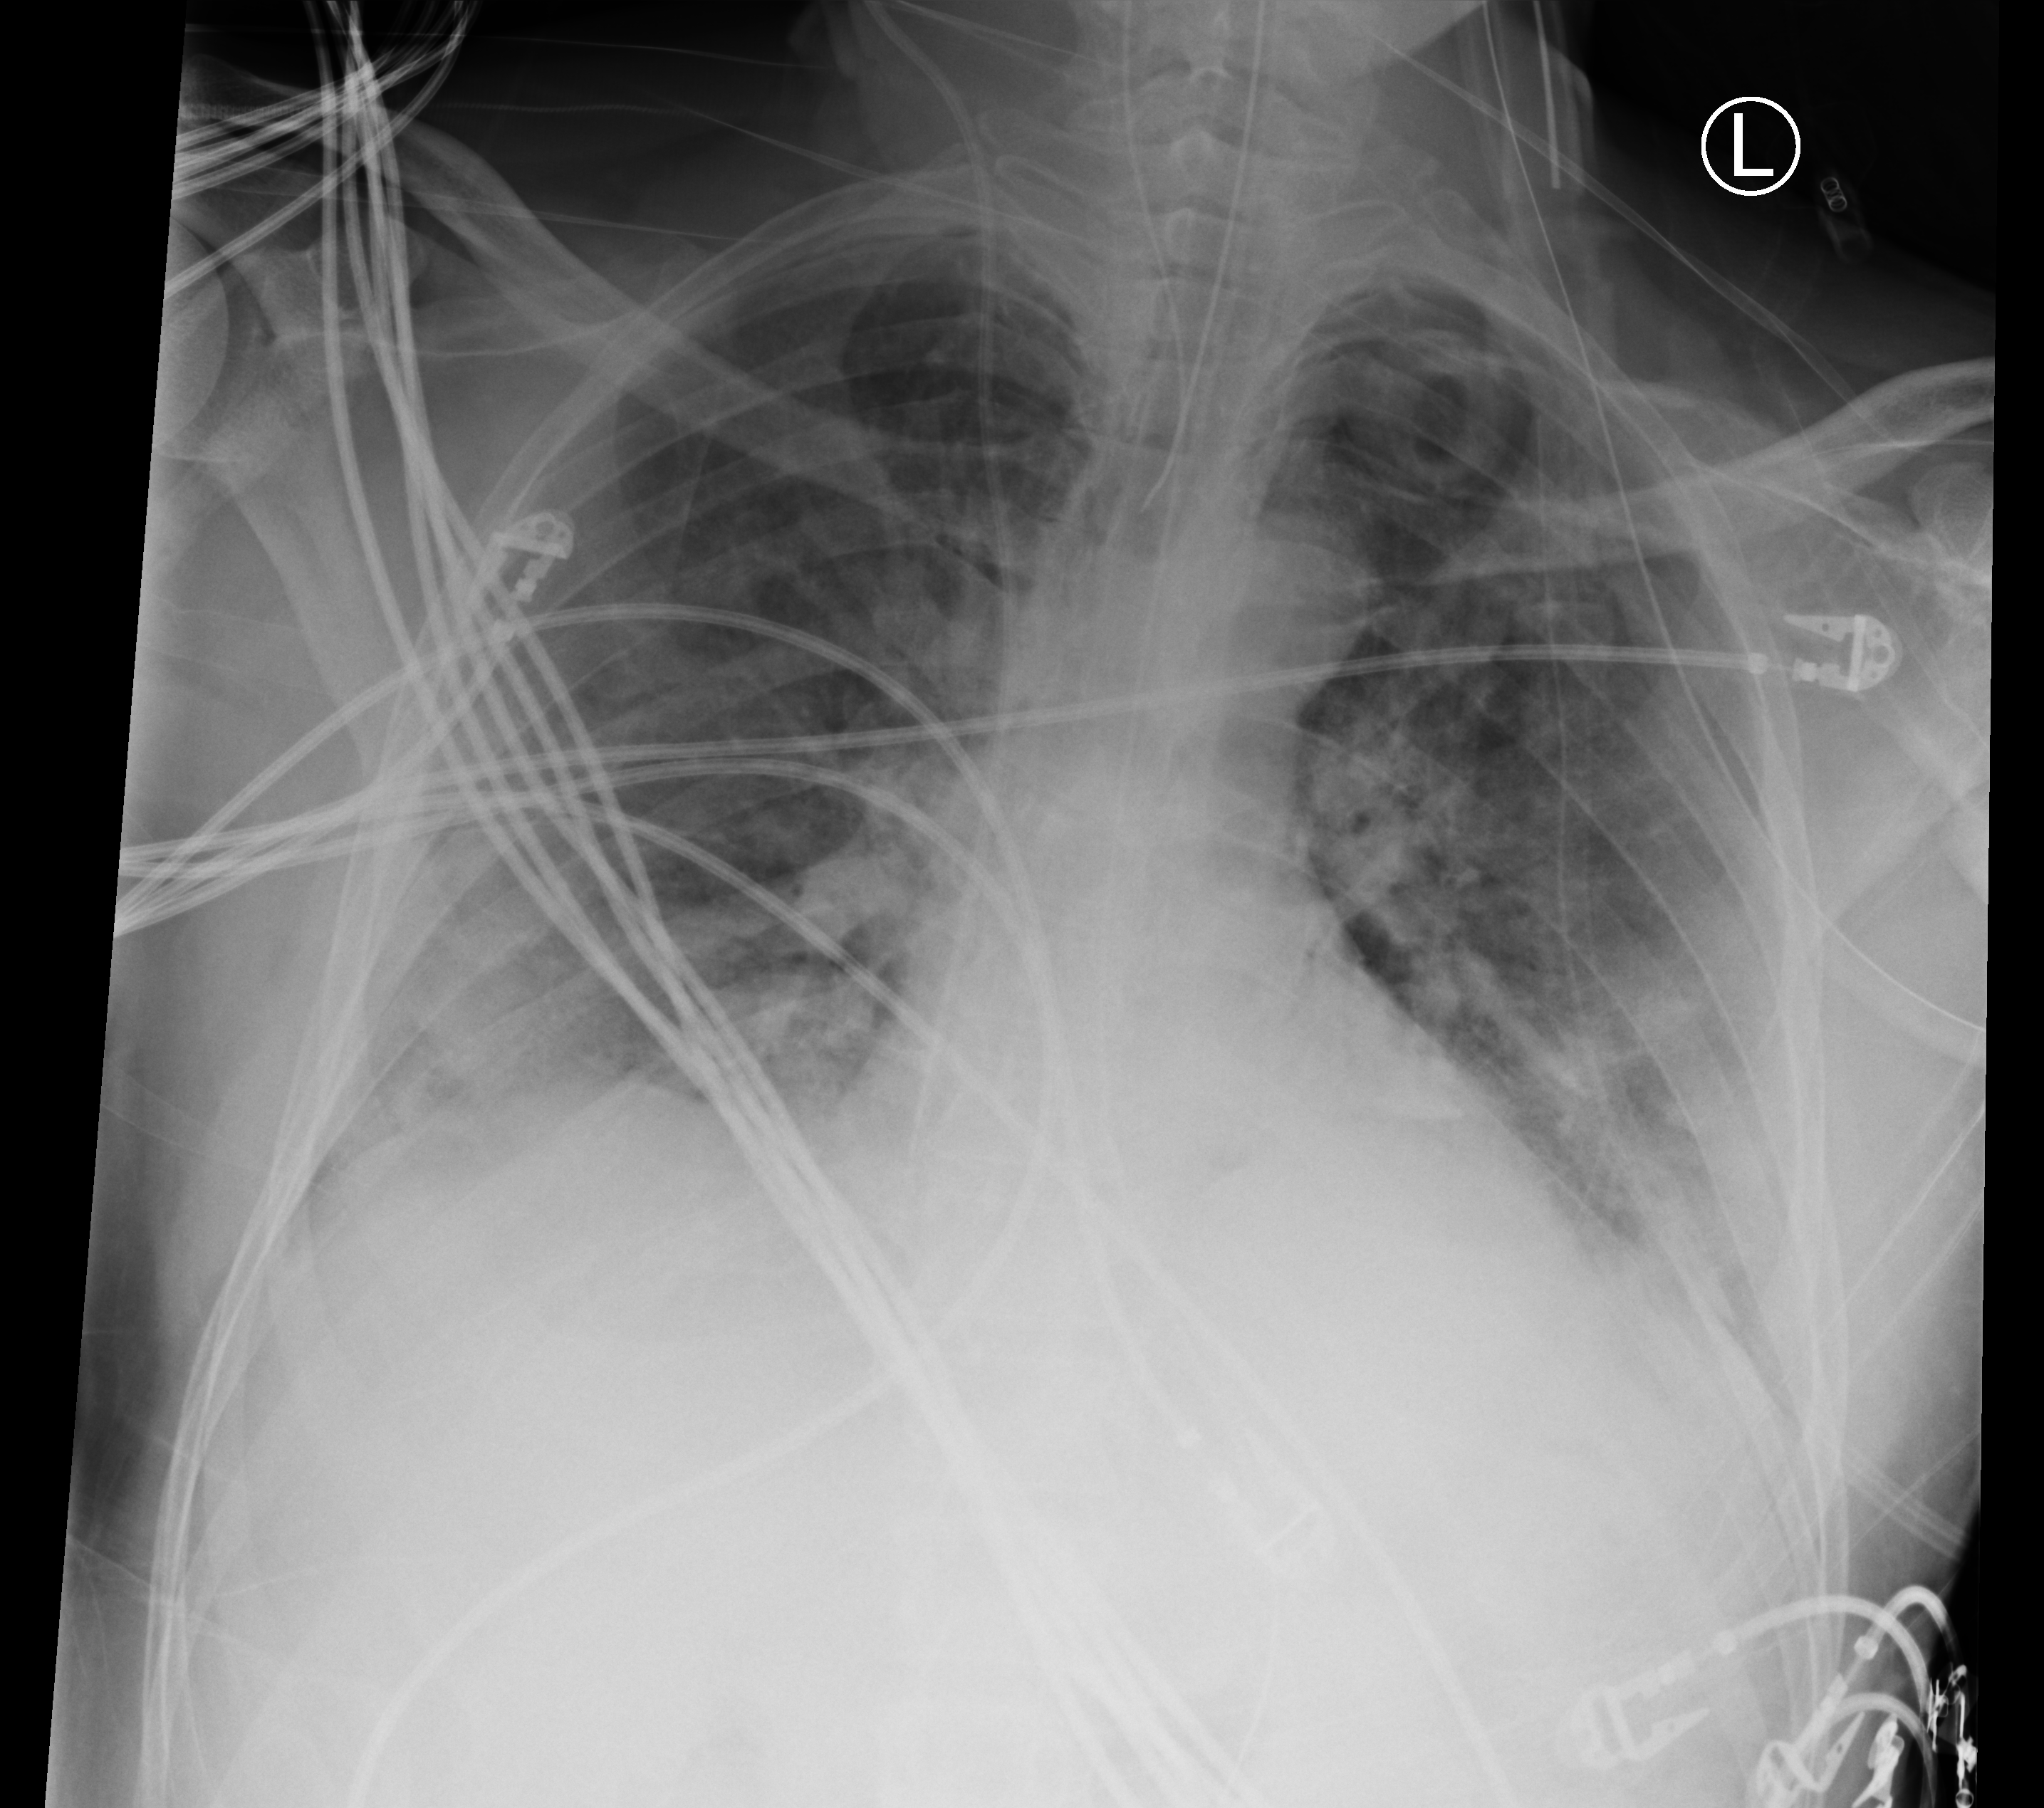
Bedside chest radiograph (computed radiography); anteroposterior (AP) projection. Male patient hospitalised with COVID-19, age 18–59 years.
Admission-level facts for this patient (not findings on this image; timing relative to this image not recorded): mechanically ventilated during this hospital stay: yes; admitted to intensive care during this hospital stay: yes; COPD (admission record): no.